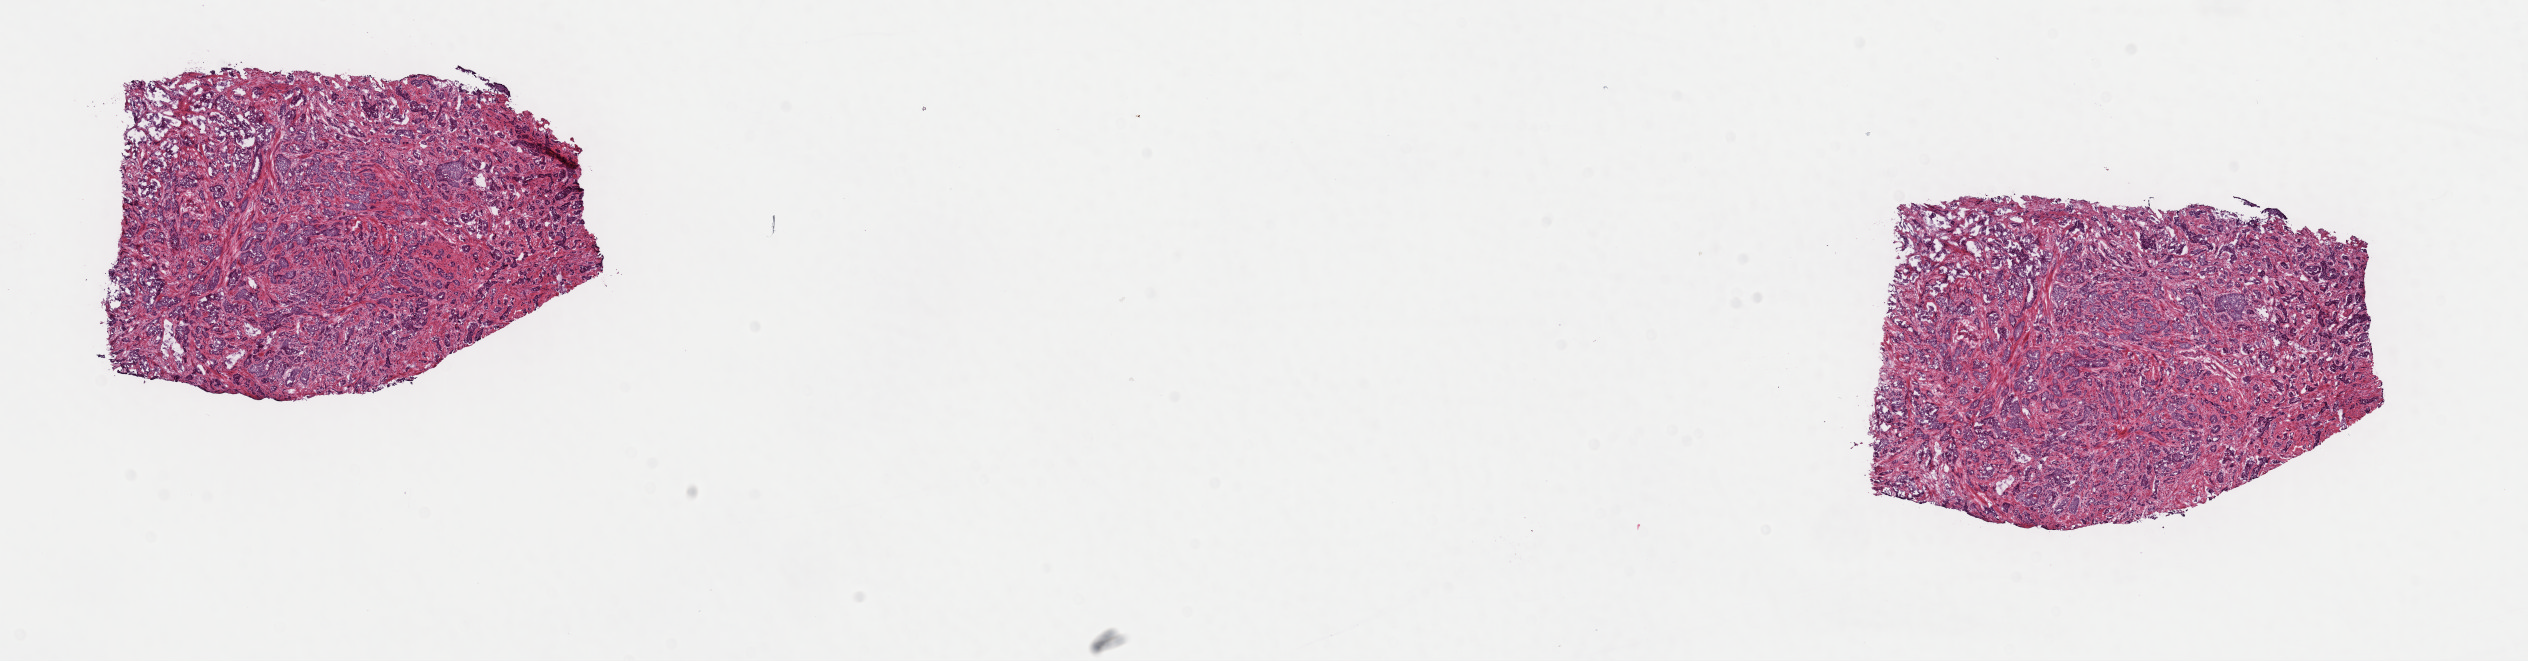
H&E-stained whole-slide image — low-resolution overview of the scanned area, about 20.0 x 5.2 mm, frozen section from the top of the tissue portion, prostate, primary tumour sample. Male patient; age at initial diagnosis 67 years. Gleason score: 9 (4+5). Pathologist review of this section (percent, as recorded): tumour cells 65%, tumour nuclei 80%, normal cells 0%, stromal cells 35%, necrosis 0%. Infiltration values recorded for this section: lymphocyte infiltration 0%, monocyte infiltration 0%, neutrophil infiltration 0%.
Histologic diagnosis: Adenocarcinoma, NOS (prostate gland). Laterality: bilateral.